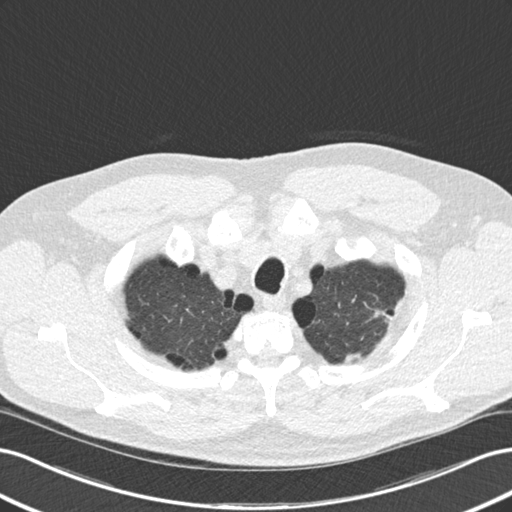
Low-dose screening chest CT, one axial slice; position 146 of 177 along the scan axis; reconstruction kernel B30f; lung window (W 1500 / L -600 HU); 2 mm slice thickness; 512 × 512 image matrix, field of view 360 × 360 mm.
Outlined on this slice (expert manual segmentation):
- lesion 1 (tumor, upper lobe of left lung): bounding box [x1, y1, x2, y2] px = [374, 309, 391, 321]